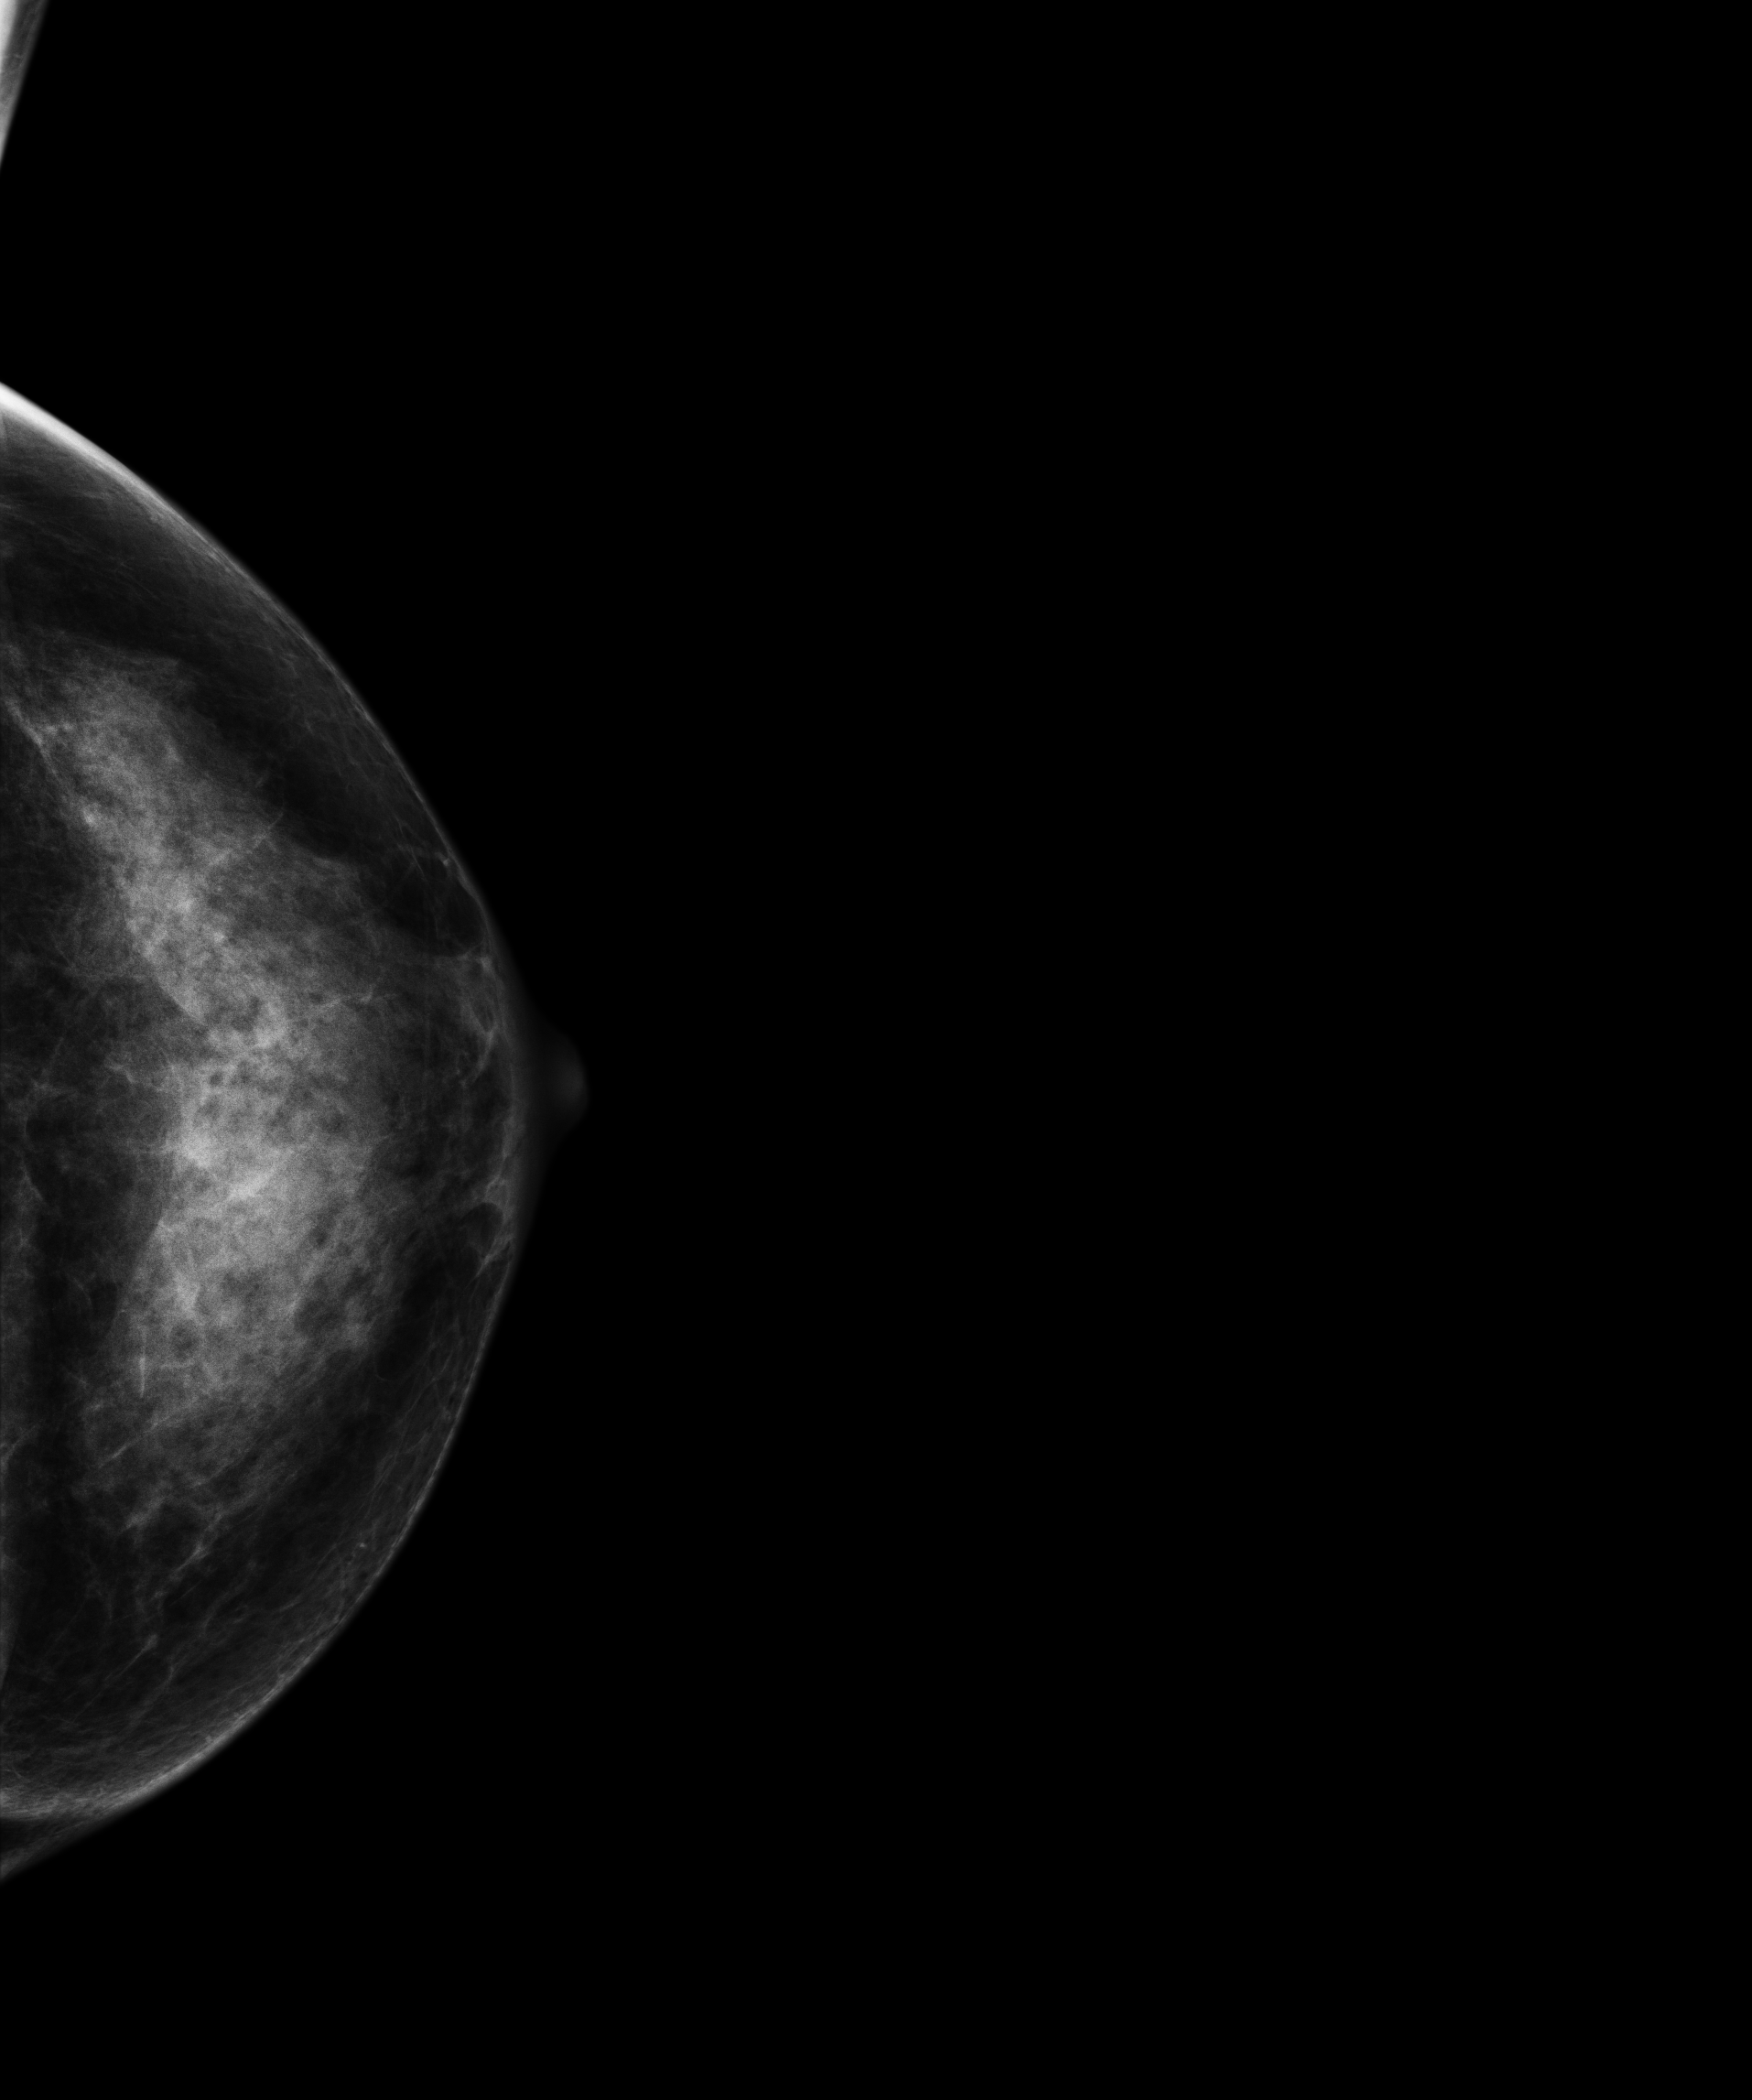
Screening examination. Patient: female, 56 years.
Image type: full-field digital mammogram. Breast: left. Projection: cranio-caudal projection.